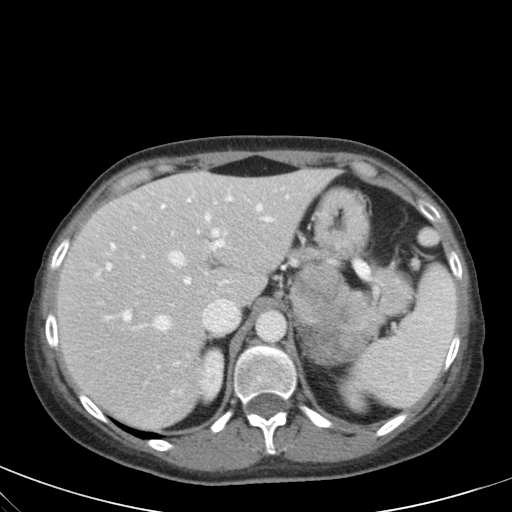
Contrast-enhanced abdominal CT, one axial slice. Position 43 of 59 along the scan axis. 120 kVp. Intravenous contrast given. Soft-tissue window (W 400 / L 40 HU). 4 mm slice thickness. 512 × 512 image matrix, field of view 350 × 350 mm. Female patient, age 28 years. Case-level facts recorded for this patient, not image findings: diagnosis: adrenocortical carcinoma; tumour side: left adrenal; tumour size at pathology: 7 cm; Ki-67 index: 40 %; stage (as recorded): 4.
Annotated regions visible in this slice (semi-automatically segmented with operator editing):
- mass: box from (x=292, y=262) to (x=384, y=364) px